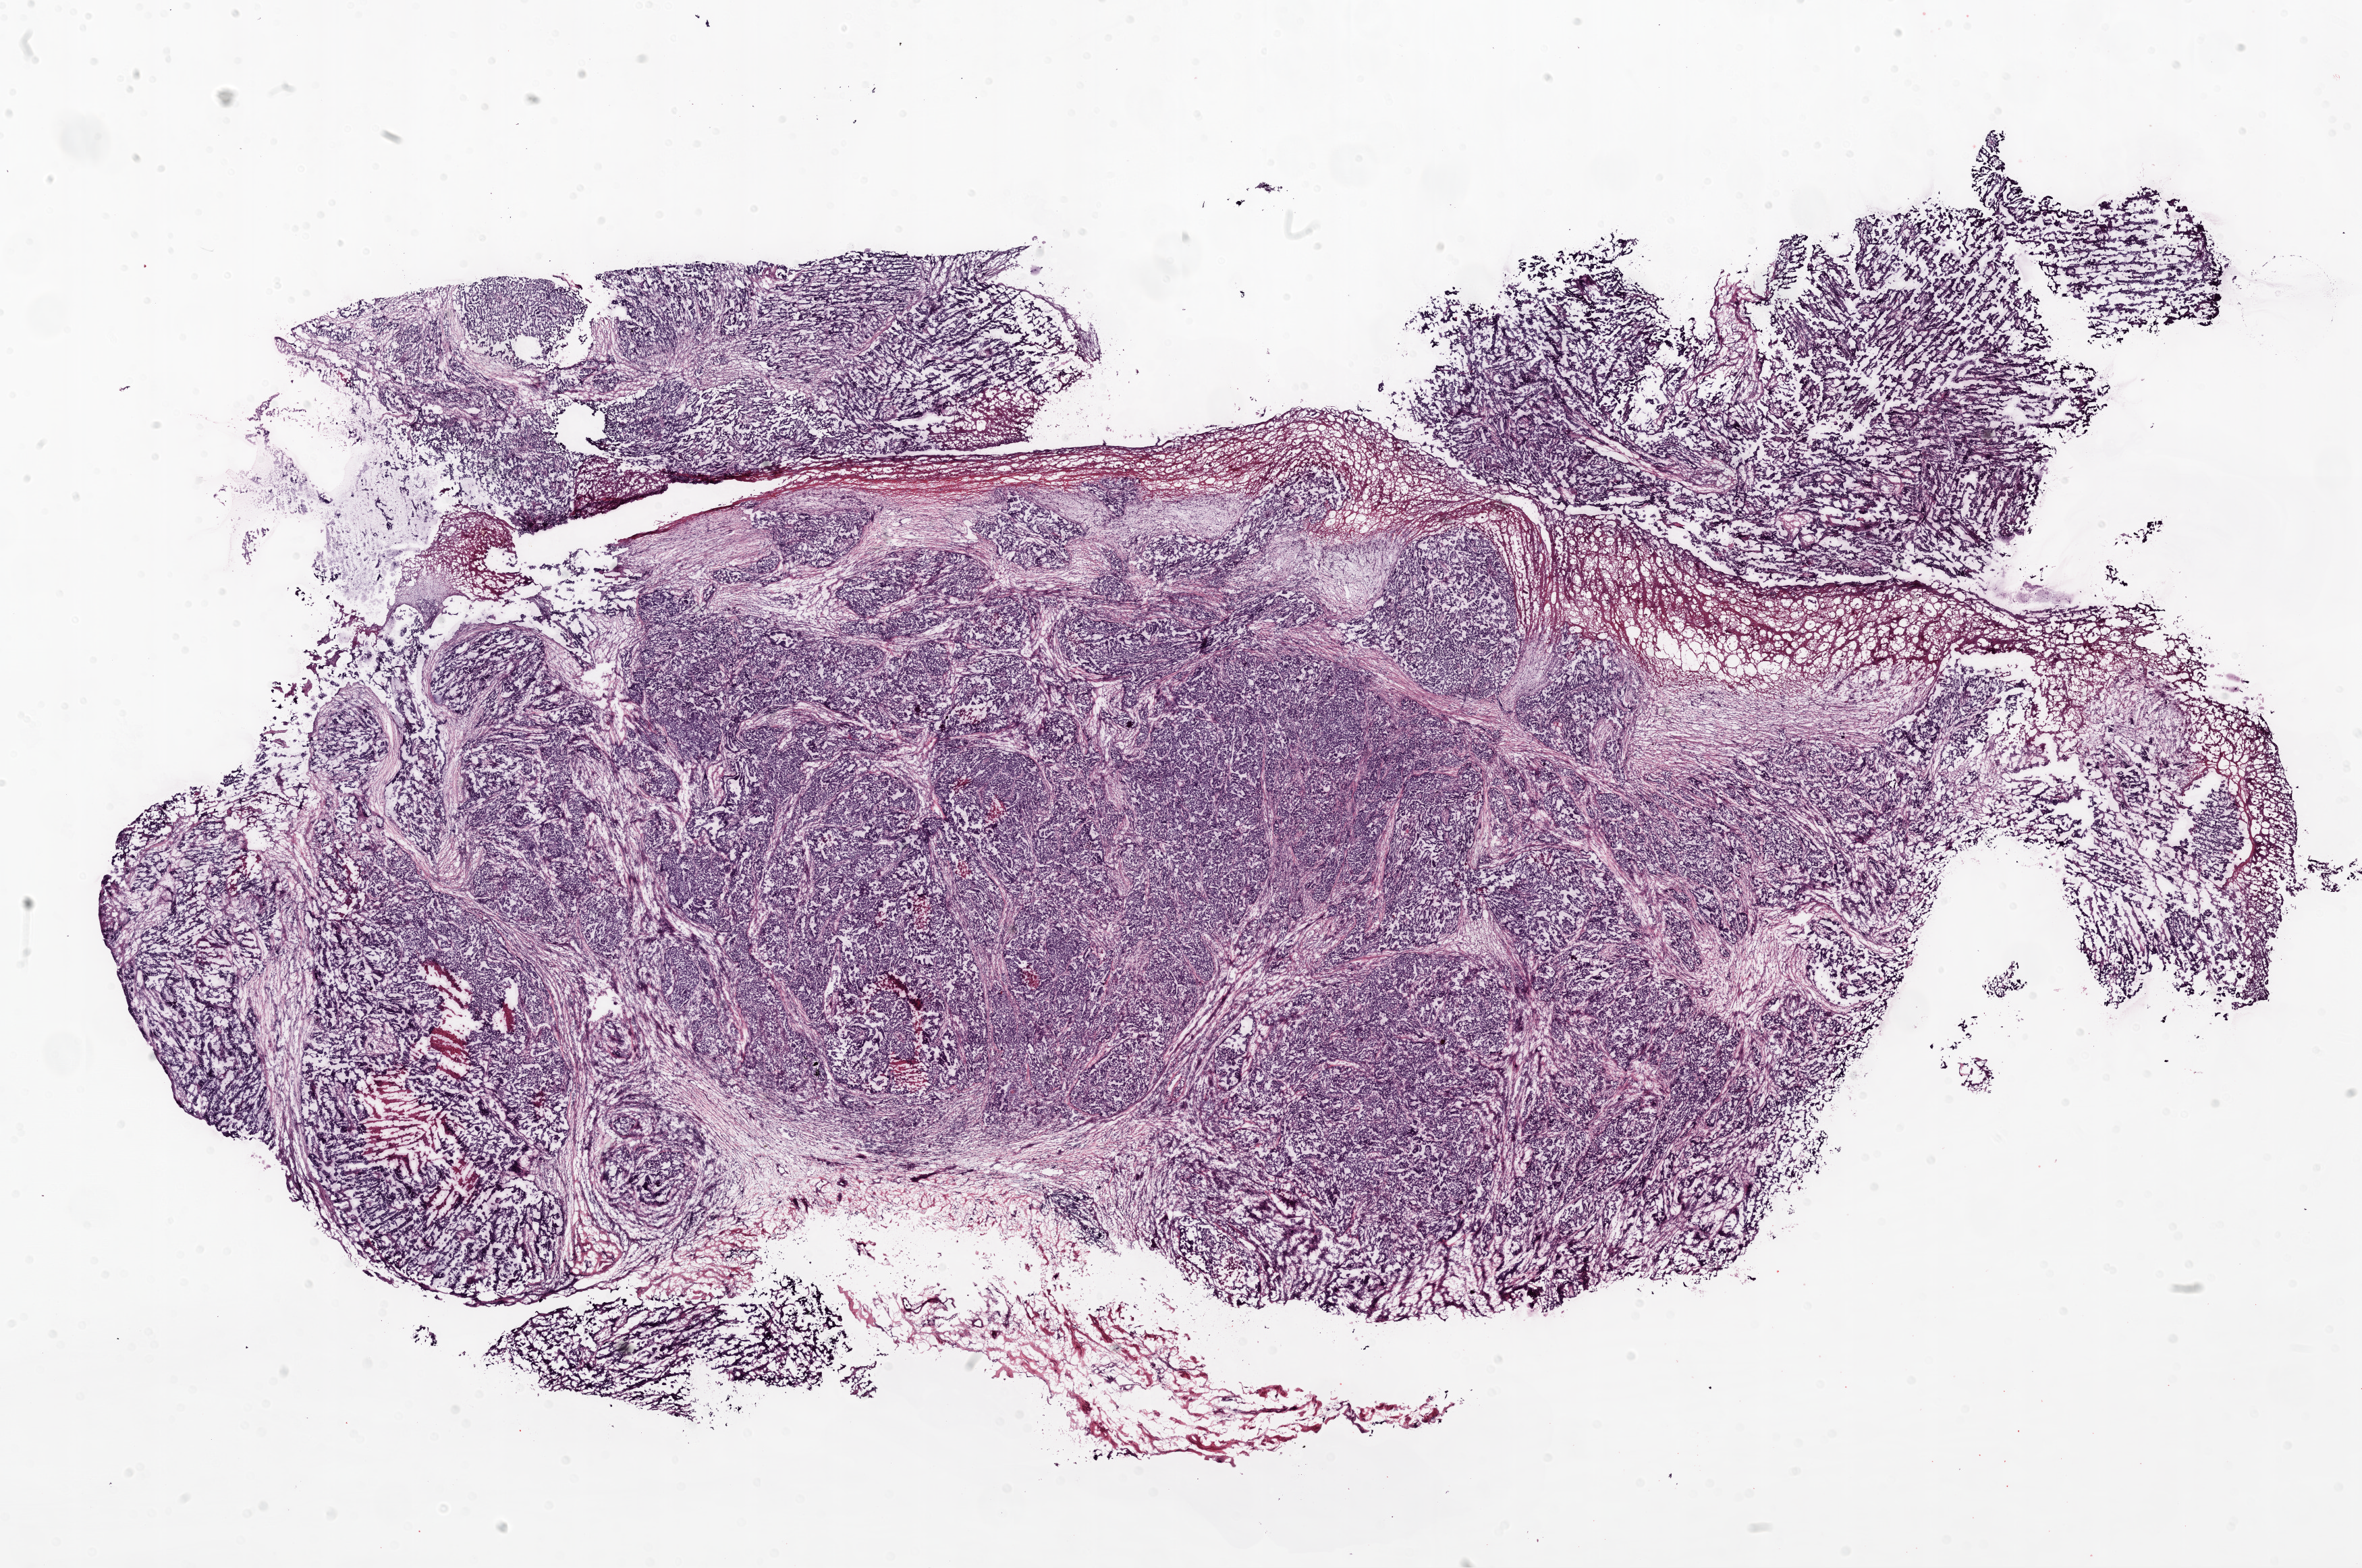
H&E whole-slide image, a low-resolution overview of the entire scanned area, about 28.1 x 18.6 mm (acquisition: 20x scan). Frozen section from the top of the tissue portion. Primary tumour sample from the ovary. Female patient; age at initial diagnosis 51 years. Histologic grade: G3 (poorly differentiated). Composition of this section per pathologist review: tumour cells 85%, tumour nuclei 80%, normal cells 0%, stromal cells 10%, necrosis 5%. Inflammatory infiltration, as recorded: lymphocyte infiltration 15%, monocyte infiltration 0%, neutrophil infiltration 0%.
* FIGO stage: IV
* laterality: bilateral
* pathologic diagnosis: Serous cystadenocarcinoma, NOS